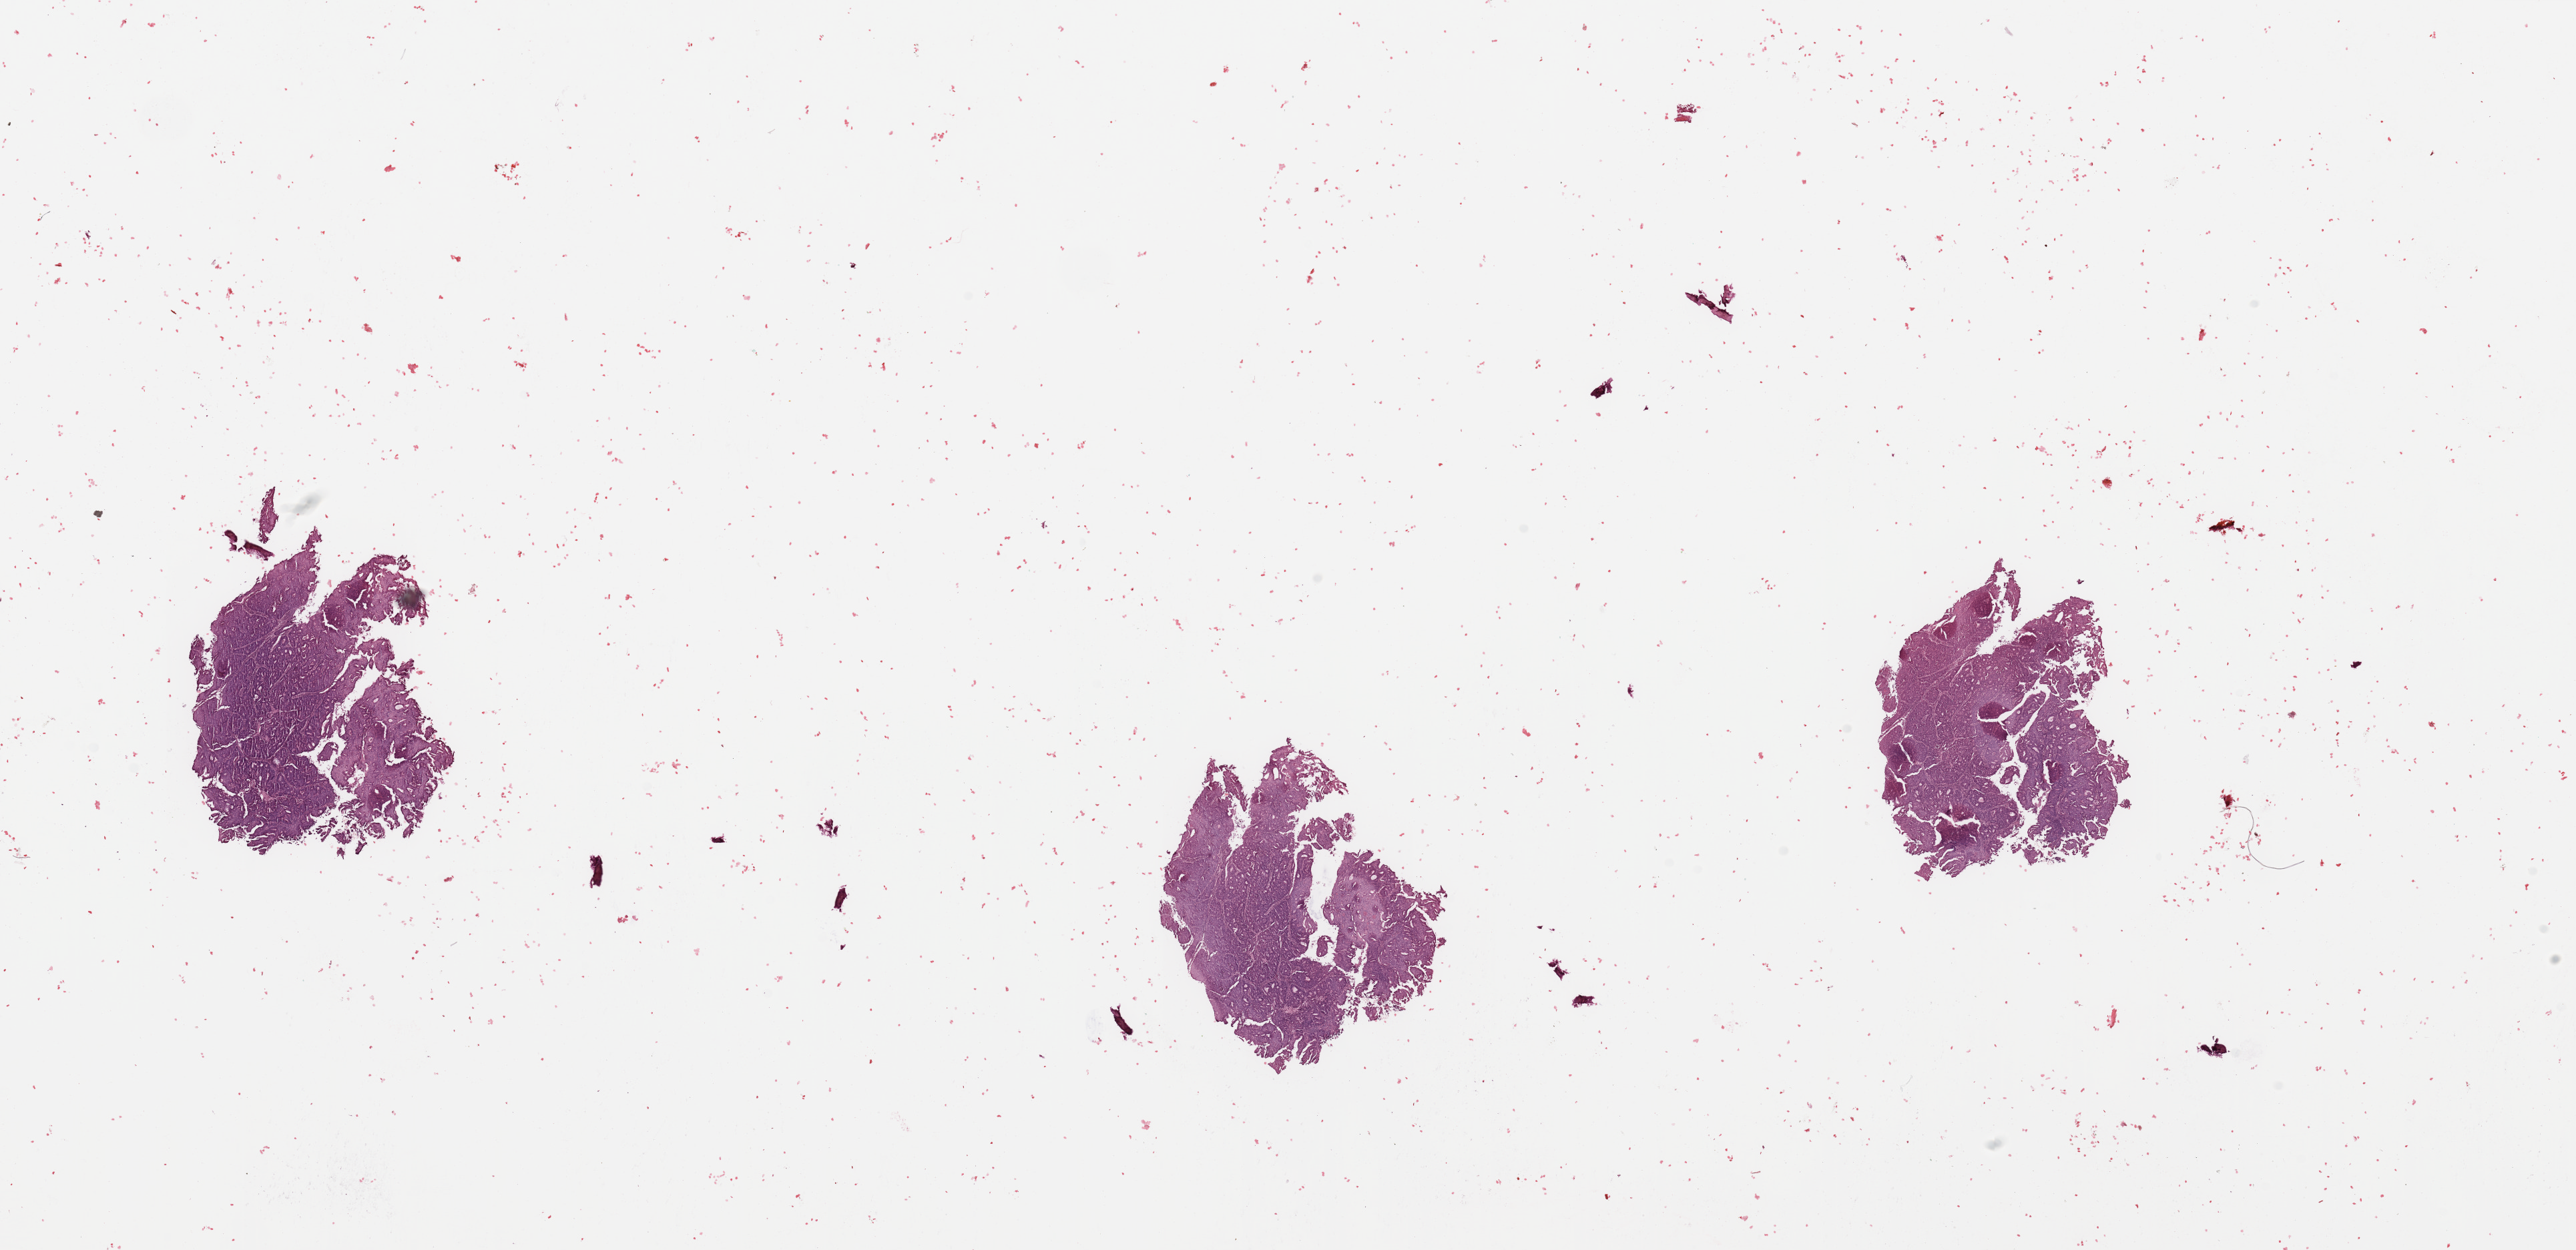
H&E-stained whole-slide image — shown as a low-resolution overview of the whole scanned area (about 30.5 x 14.8 mm, from a 20x scan); uterus, tumour tissue. 82-year-old female patient. Histologic grade: G2 (moderately differentiated).
- histologic diagnosis: Endometrioid adenocarcinoma, NOS
- AJCC pathologic stage: I
- primary tumour site (as recorded): anterior endometrium